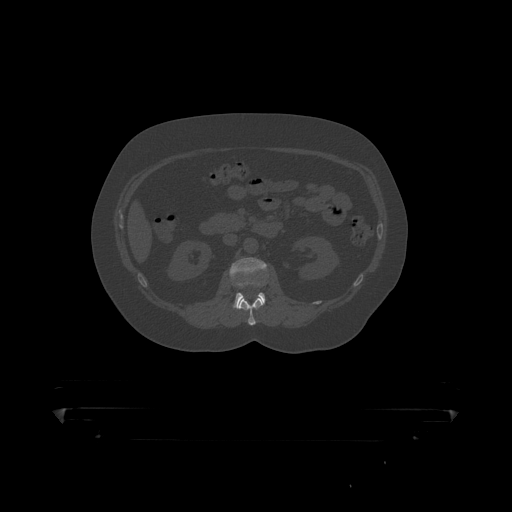
CT including the spine, one axial slice; slice 131 of 390 in the series (ordered by position); reconstruction kernel STANDARD; bone window (W 1800 / L 400 HU); 1.25 mm slice thickness; 512 × 512 image matrix, field of view 650 × 650 mm. Male patient, age 60 years. Case-level facts recorded for this patient, not image findings: primary cancer: prostate.
Structures marked on this image (semi-automatic segmentation, software-assisted and operator-edited):
- L1 vertebra: bounding box [x1, y1, x2, y2] px = [239, 299, 264, 319]
- L2 vertebra: [230, 257, 267, 310]